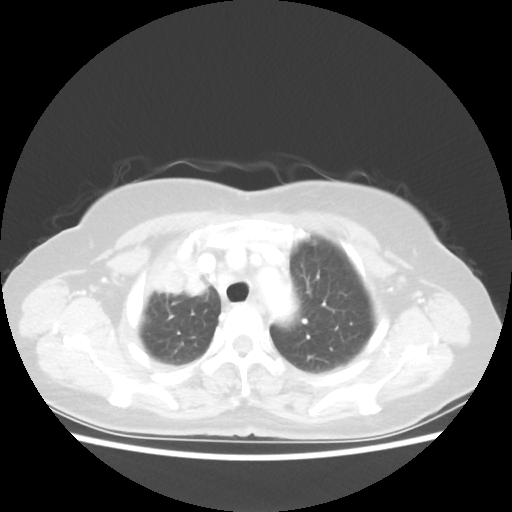
Chest CT, one axial slice. Position 43 of 55 along the scan axis. 80 kVp. Lung window (W 1500 / L -600 HU). 5 mm slice thickness. 512 × 512 image matrix, field of view 337 × 337 mm. Patient: female, 62 years. From the clinical record (not read from this slice): clinical TNM (as recorded): T4 N3 M0.
Structures marked on this image (bounding box drawn by a radiologist):
- lung tumour (recorded histology: squamous cell carcinoma): bounding box [x1, y1, x2, y2] px = [143, 245, 213, 301]